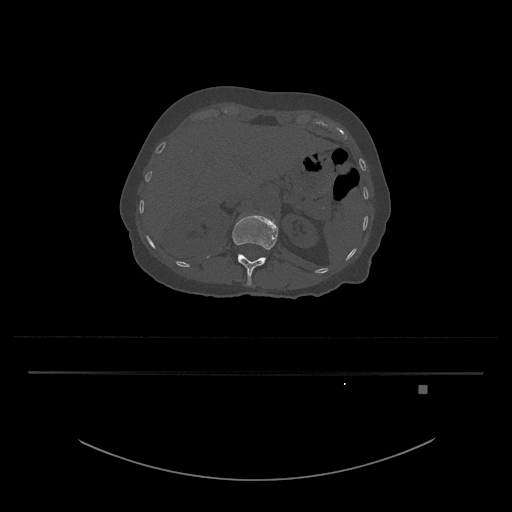
CT including the spine, one axial slice; position 545 of 797 along the scan axis; reconstruction kernel Br40s/3; bone window (W 1800 / L 400 HU); 512 × 512 image matrix. Female patient, age 57 years. From the clinical record (not read from this slice): primary cancer: cervical.
Outlined on this slice (semi-automatically segmented with operator editing):
- L1 vertebra: bounding box (x1, y1, x2, y2) in pixels: (207, 215, 278, 286)